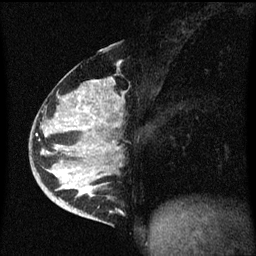
Breast MRI (dynamic contrast-enhanced), one sagittal slice. Slice 27 of 60 in the series (ordered by position). Dynamic contrast-enhanced series, image 2 of 3 at this slice position (ordered by acquisition). 1.5 T. TE 4.2 ms, TR 8.4 ms. 256 × 256 image matrix, field of view 200 × 200 mm. Patient: female, 34 years. Case-level facts recorded for this patient, not image findings: setting: breast cancer imaged before/during neoadjuvant chemotherapy; receptor status: HR-positive, HER2-negative.
Annotated regions visible in this slice (semi-automatic segmentation, software-assisted and operator-edited):
- analysis volume of interest (the breast-tissue region the enhancement analysis was run in; not a lesion): bounding box [x1, y1, x2, y2] px = [34, 48, 125, 215]
- tumour enhancement mask (voxels above the 70 % enhancement threshold inside the analysis volume of interest): [64, 80, 111, 195]